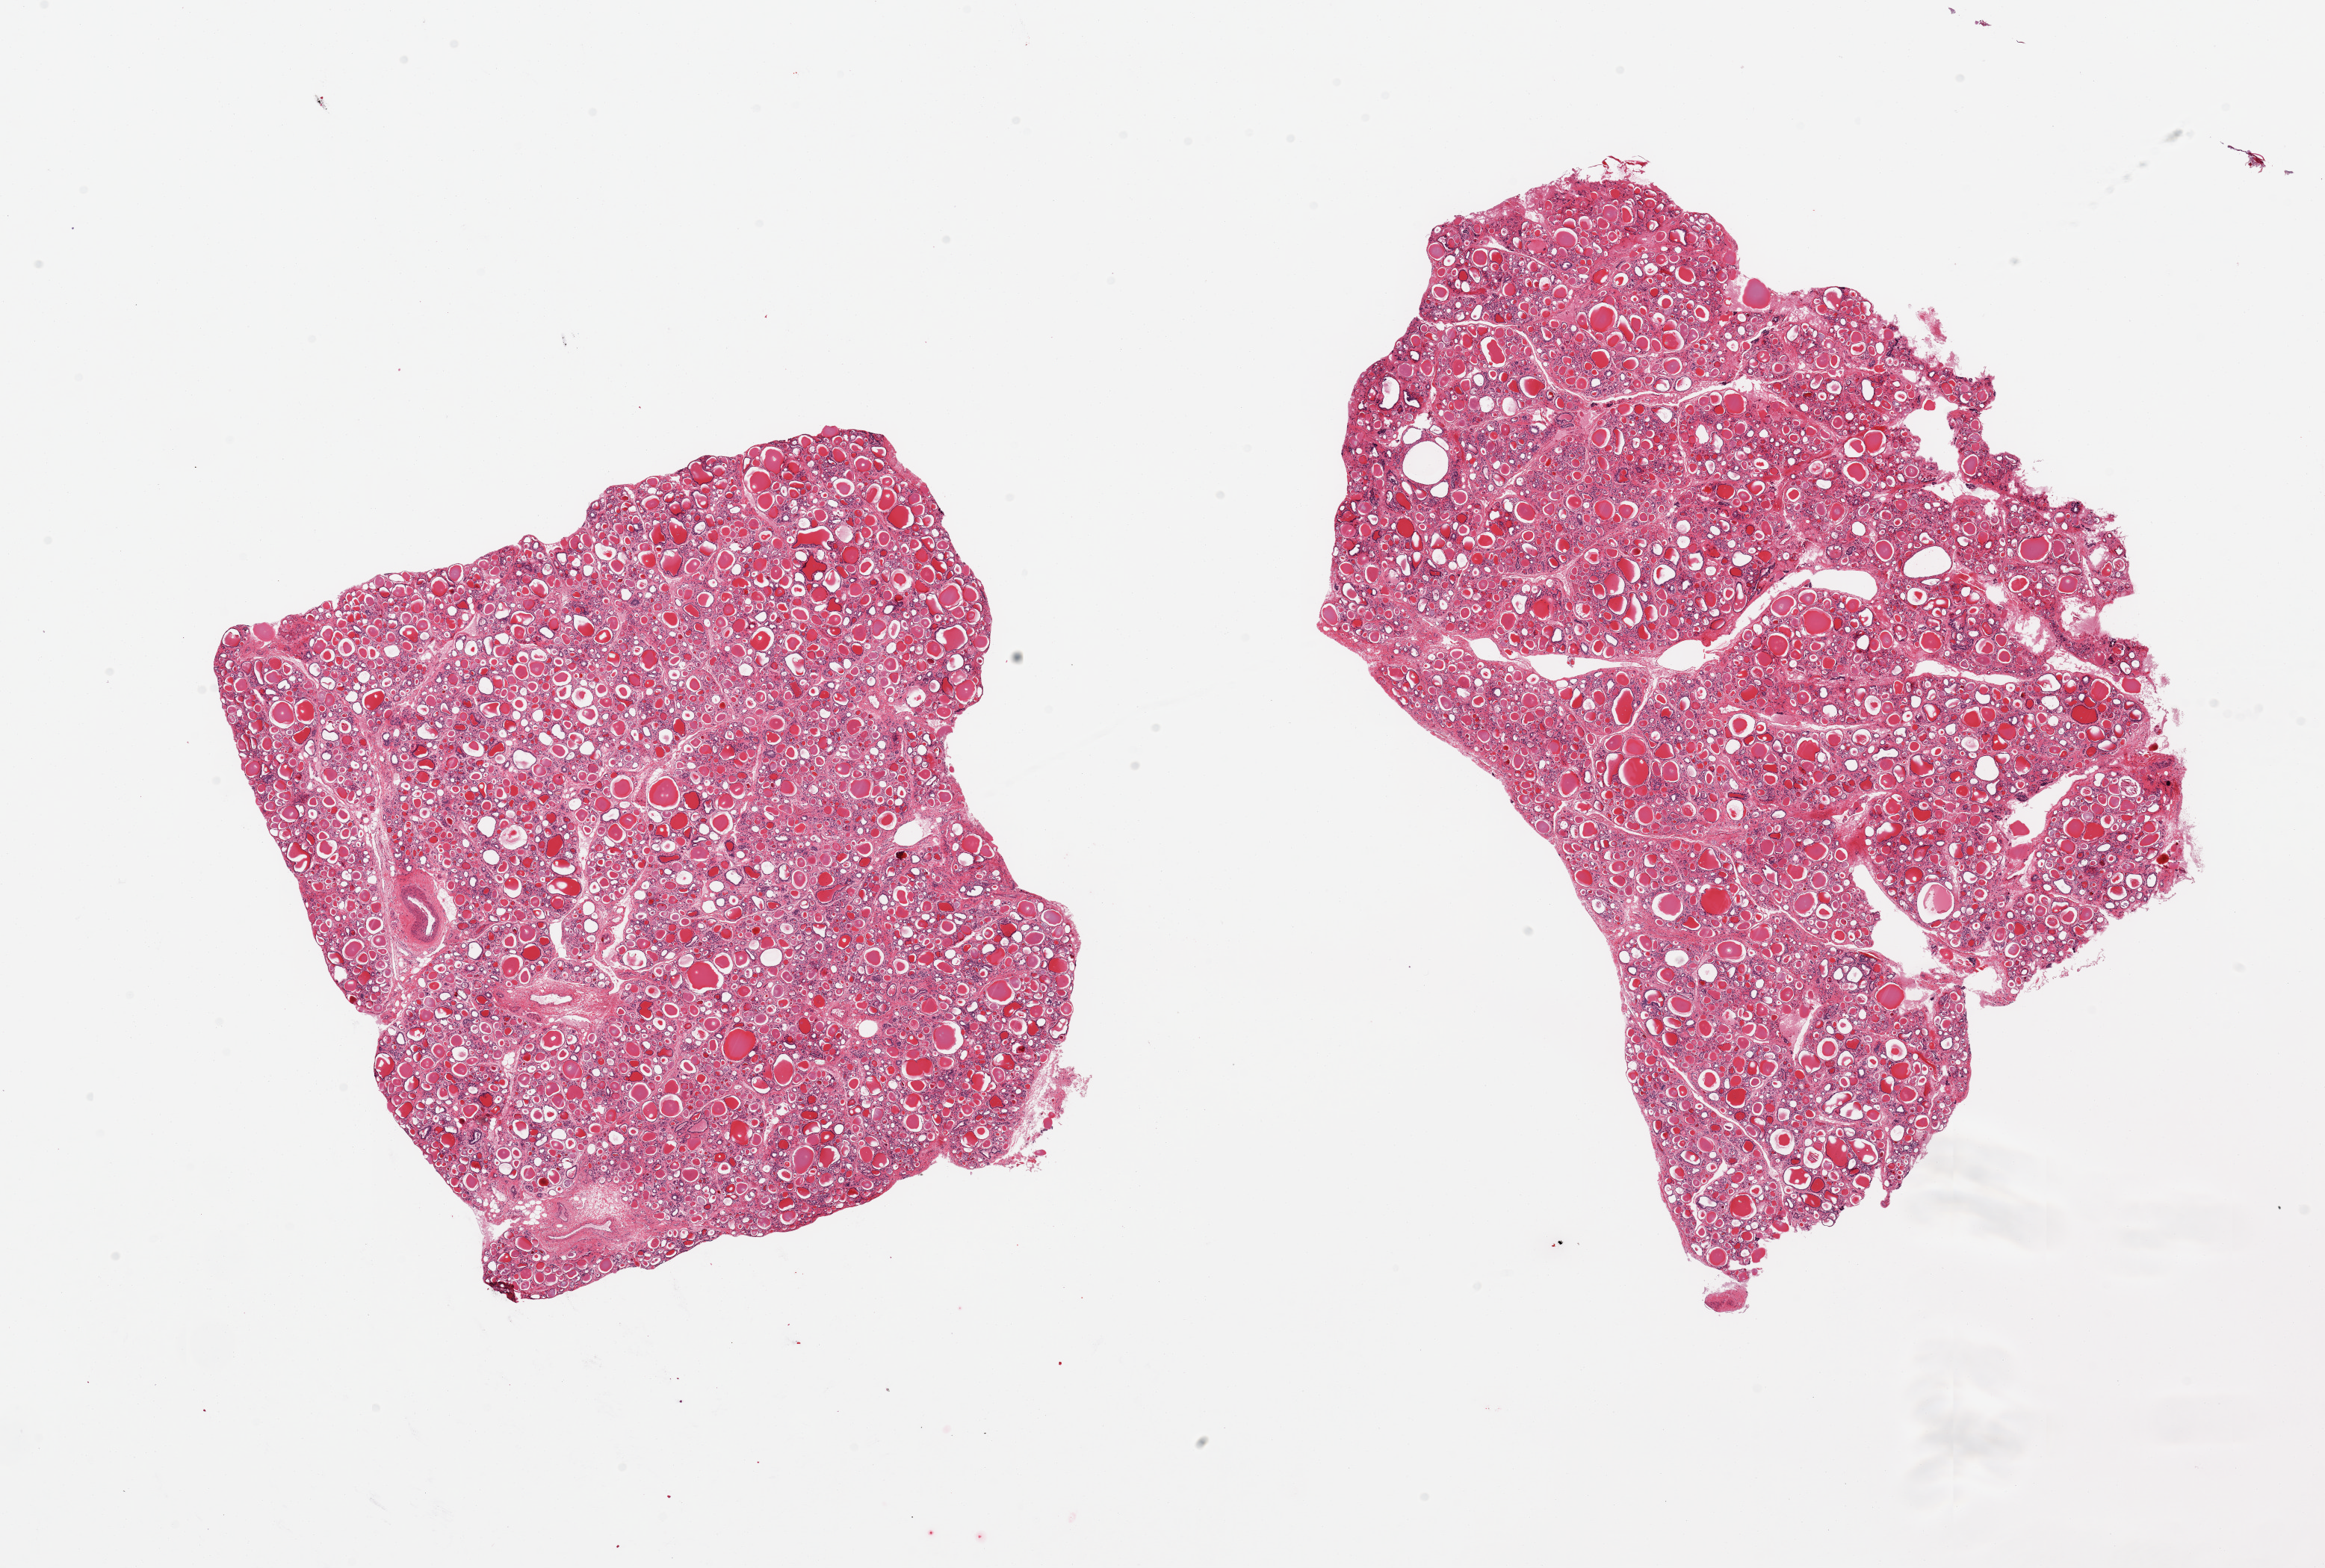
Whole-slide image, H&E stain — a low-resolution overview of the entire scanned area, about 24.6 x 16.6 mm; PAXgene-fixed, paraffin-embedded tissue; target tissue: thyroid; tissue donor sample. Male donor.
Reviewer comment on this tissue sample: 2 pieces, no abnormalities.